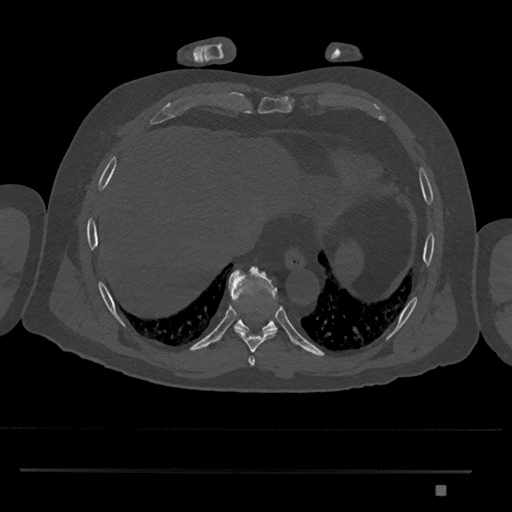
CT including the spine, one axial slice; slice 1086 of 1134 in the series (ordered by position); reconstruction kernel Br40s/3; bone window (W 1800 / L 400 HU); 0.5 mm slice thickness; 512 × 512 image matrix. Male patient, age 65 years. From the clinical record (not read from this slice): primary cancer: prostate.
Outlined on this slice (semi-automatic segmentation, software-assisted and operator-edited):
- T8 vertebra: bounding box [x1, y1, x2, y2] px = [234, 305, 276, 354]
- T9 vertebra: [228, 266, 278, 333]